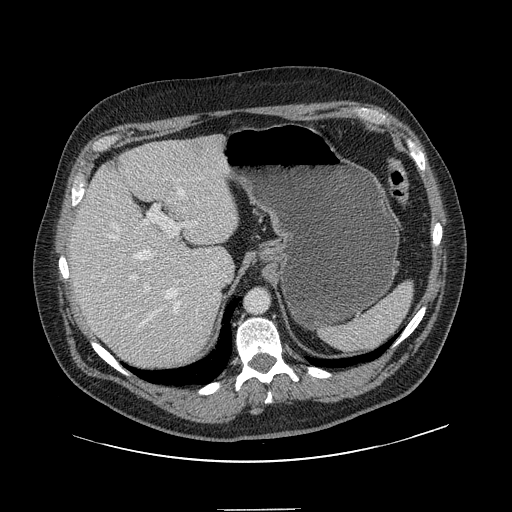
Contrast-enhanced abdominal CT, one axial slice. 120 kVp. Intravenous contrast given. Soft-tissue window (W 400 / L 40 HU). 2.5 mm slice thickness. 512 × 512 image matrix, field of view 451 × 451 mm. Male patient, age 61 years. From the clinical record (not read from this slice): diagnosis: colorectal cancer liver metastases, imaged before liver resection; multiple liver metastases: yes; largest metastasis: 2.6 cm; disease in both lobes: yes.
Annotated regions visible in this slice (outlined manually by an expert reader):
- hepatic veins: box from (x=108, y=187) to (x=185, y=327) px
- liver: (x=70, y=136)–(x=239, y=370)
- planned liver remnant (the part of the liver to remain after resection): (x=70, y=144)–(x=240, y=359)
- portal vein (with intrahepatic branches): (x=125, y=204)–(x=197, y=318)
- liver metastasis: (x=191, y=143)–(x=202, y=152)